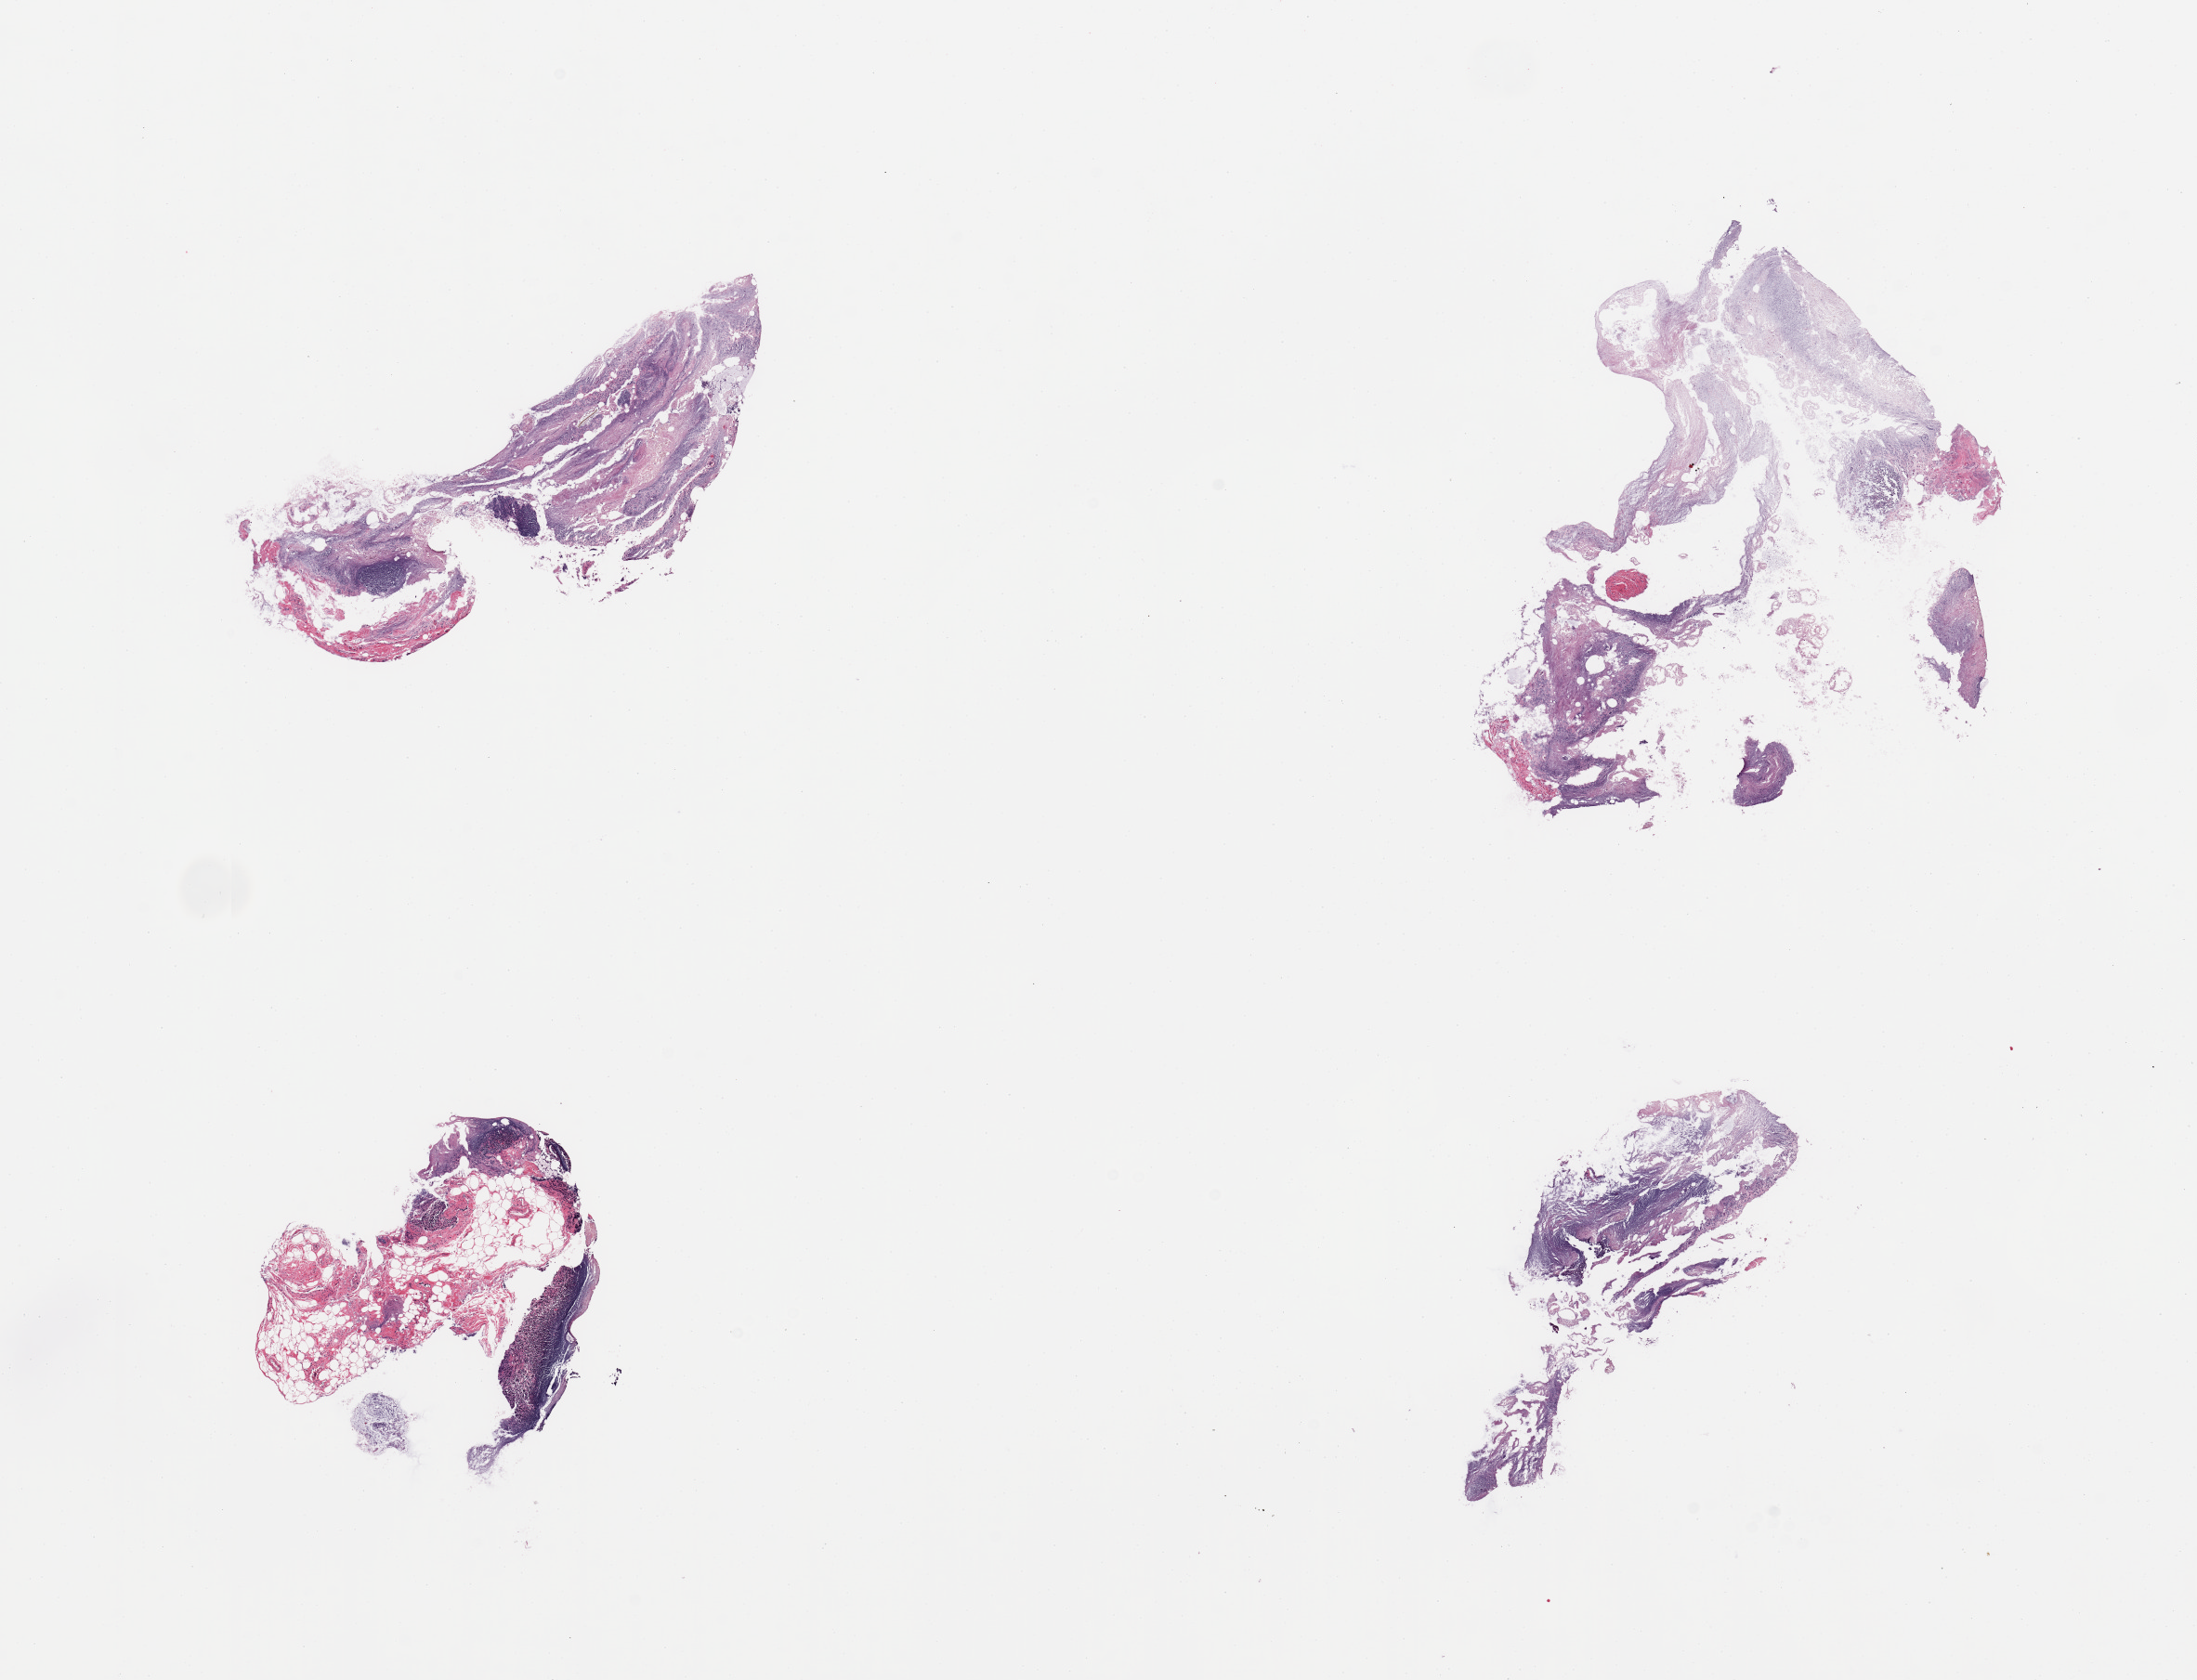
Whole-slide image, haematoxylin and eosin stain — shown as a low-resolution overview of the whole scanned area (about 18.7 x 14.3 mm). PAXgene-fixed paraffin-embedded (PFPE) section. Section of ileum (target tissue). Tissue donor sample. Donor sex: male.
• pathologist's review note for this sample: 4 pieces, mucosa with advanced autolysis; ~10% retained lymphoid aggregates